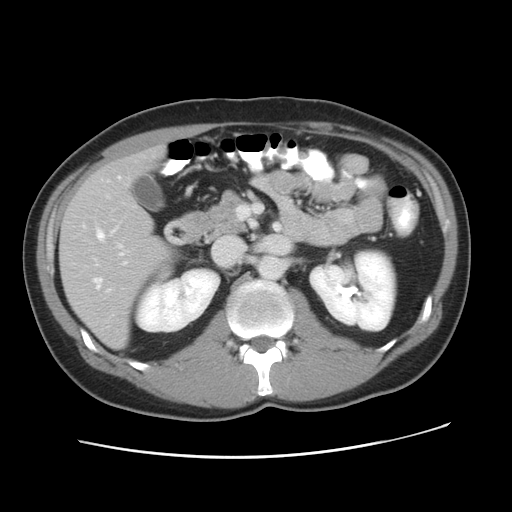
Contrast-enhanced abdominal CT, one axial slice. Slice 24 of 49 in the series (ordered by position). Reconstruction kernel STANDARD. 120 kVp. Intravenous contrast given. Soft-tissue window (W 400 / L 40 HU). 5 mm slice thickness. 512 × 512 image matrix. Male patient, age 41 years. Case-level facts recorded for this patient, not image findings: diagnosis: colorectal cancer liver metastases, imaged before liver resection; multiple liver metastases: yes; largest metastasis: 0.7 cm; disease in both lobes: yes.
Structures marked on this image (manually delineated by an expert):
- hepatic veins: bounding box (x1, y1, x2, y2) in pixels: (94, 177, 122, 288)
- liver: (60, 149, 171, 347)
- planned liver remnant (the part of the liver to remain after resection): (112, 149, 163, 183)
- portal vein (with intrahepatic branches): (107, 247, 126, 291)